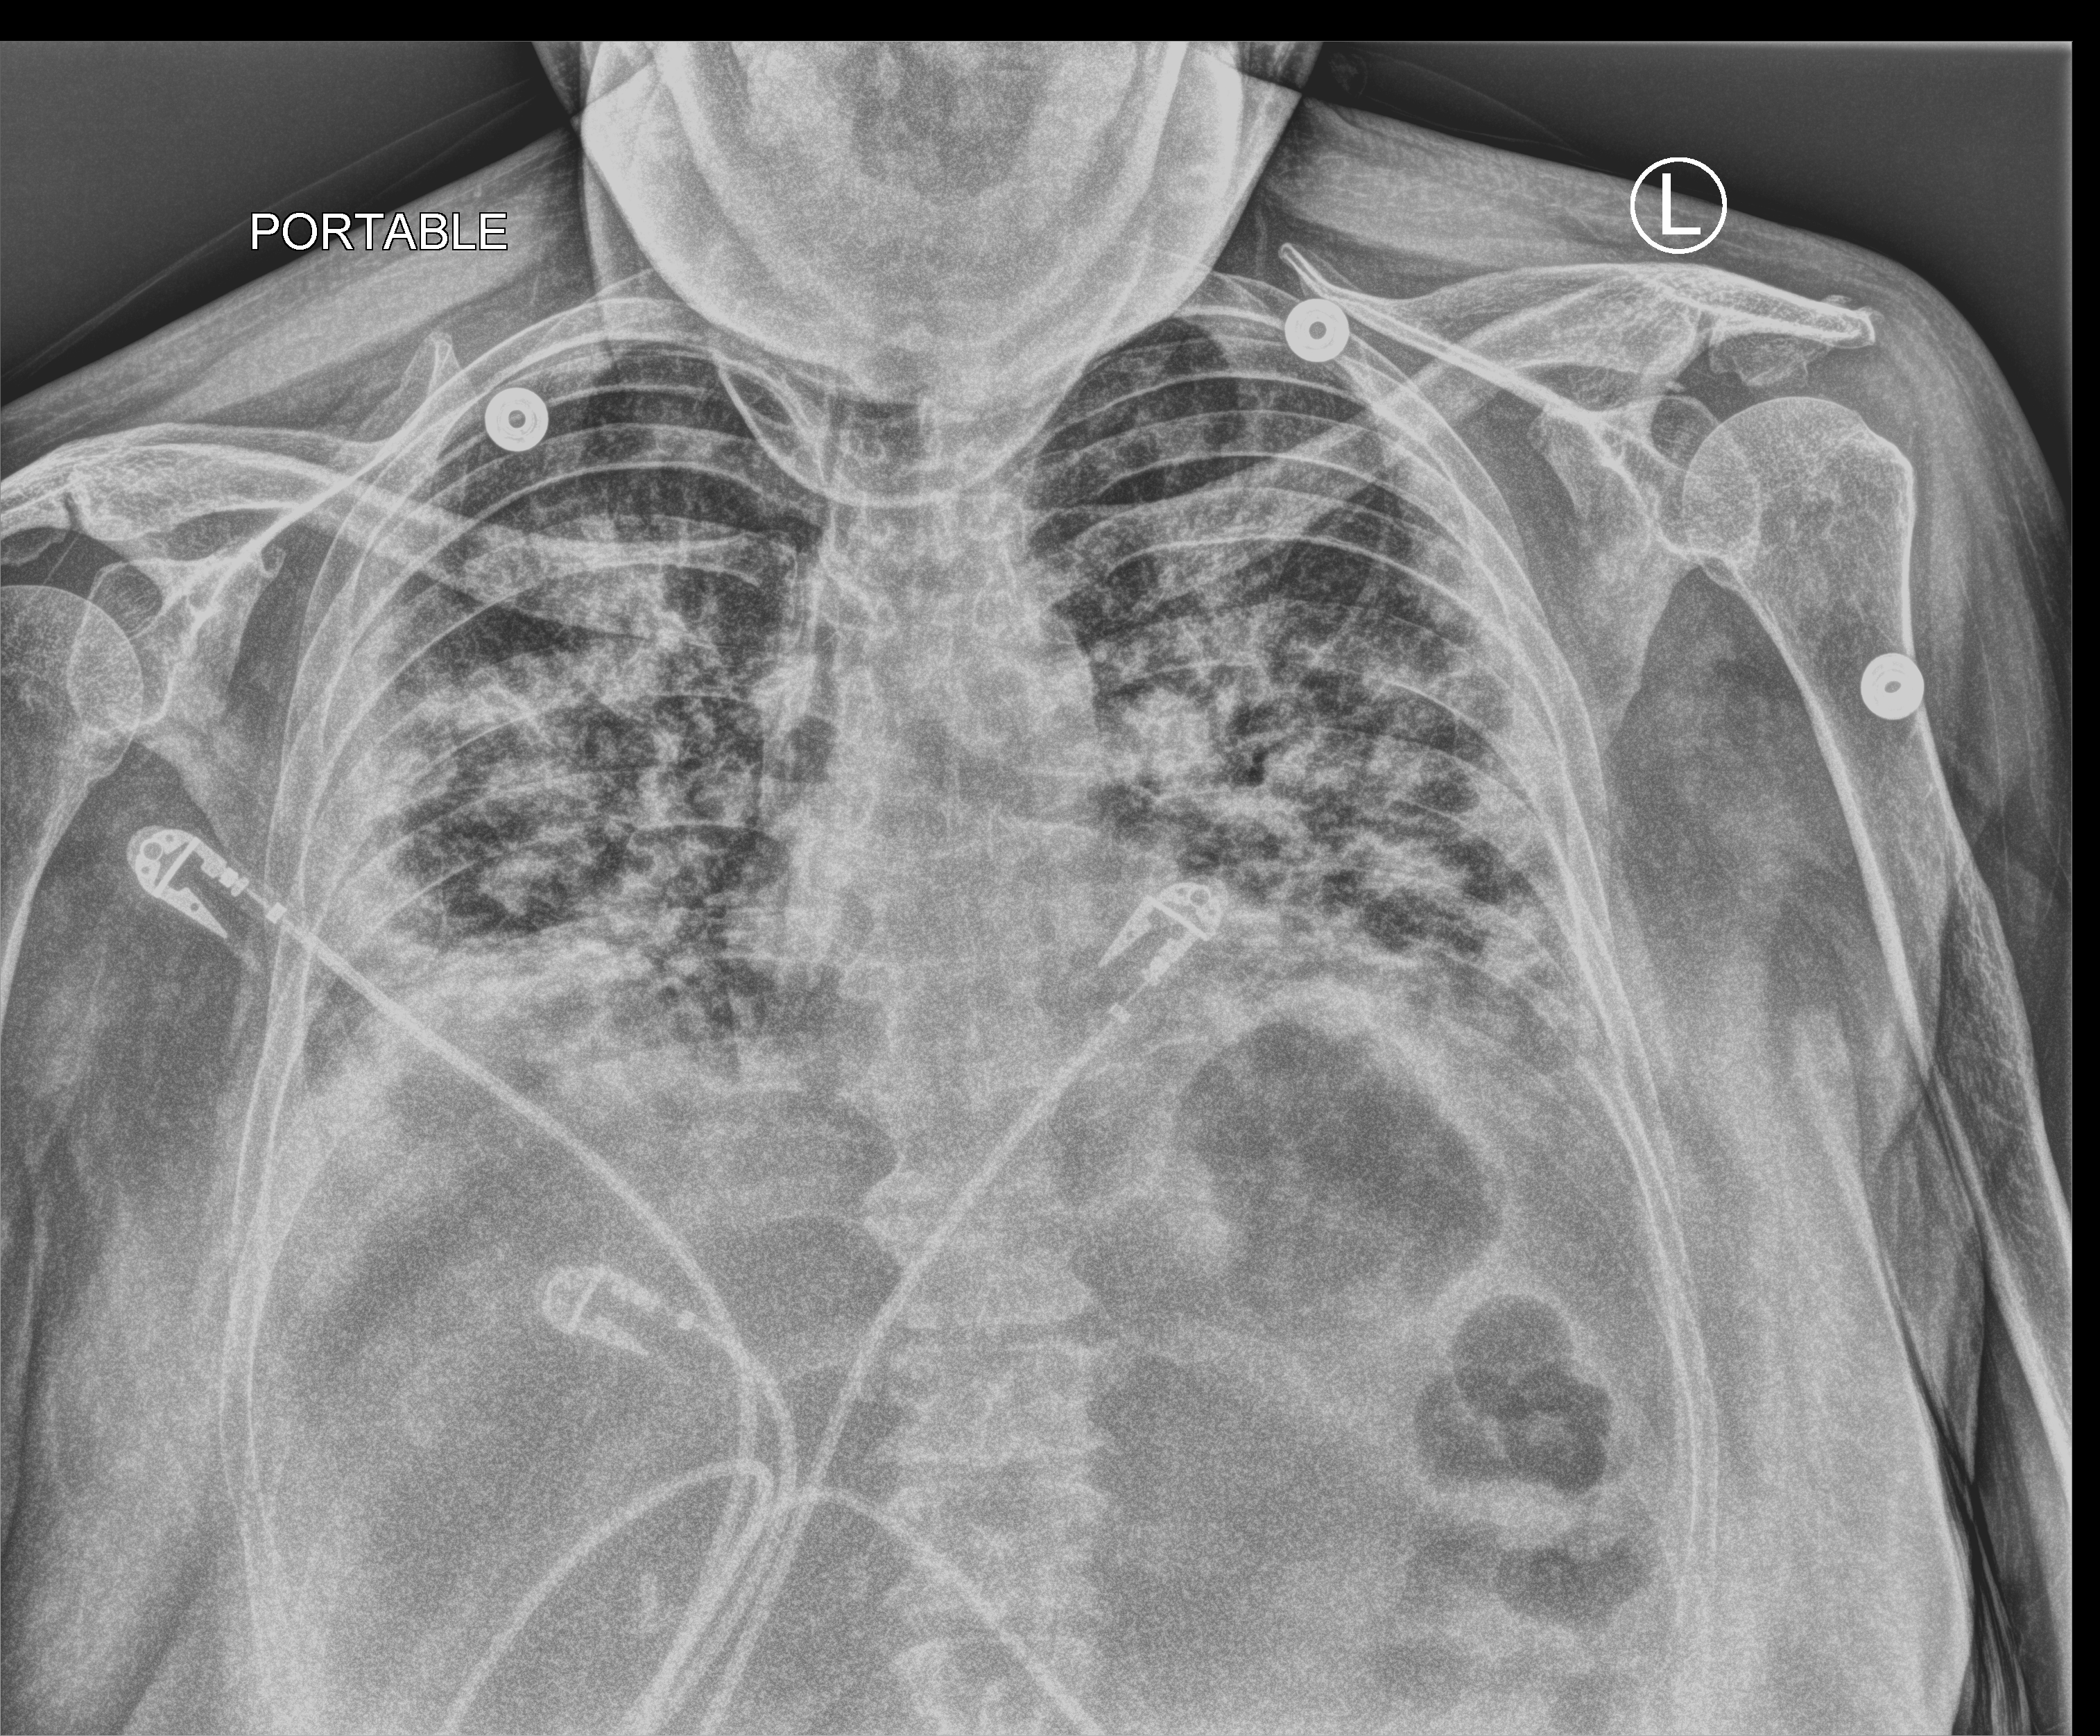
Bedside chest radiograph (computed radiography). Patient hospitalised with COVID-19; female, aged 18–59 years.
Hospital-stay facts (about this admission, not read from this image; timing relative to this image not recorded): mechanically ventilated during this hospital stay: no; COPD (admission record): no; admitted to intensive care during this hospital stay: yes.